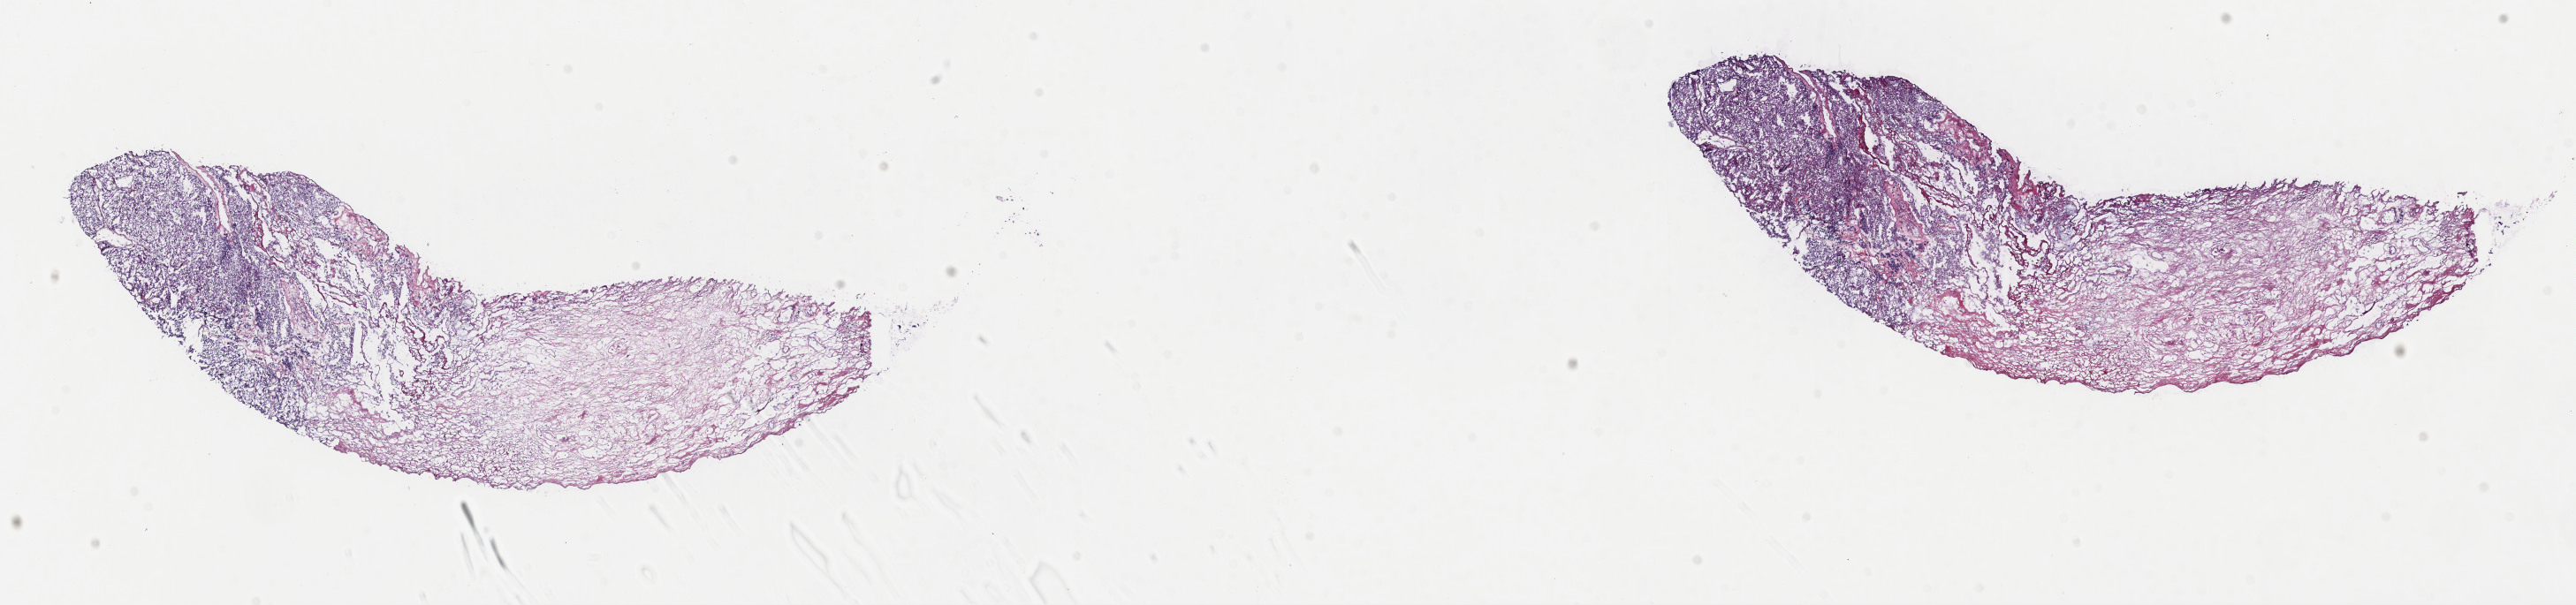
Whole-slide histology image, Hematoxylin and eosin (H&E) stained — low-resolution overview of the scanned area, about 23.0 x 5.4 mm (acquisition: 40x scan), frozen section from the top of the tissue portion, primary tumour sample from the kidney. Patient: male, age at initial diagnosis 48 years. Histologic grade: G3 (poorly differentiated). Slide review estimates, as recorded: tumour cells 50%, tumour nuclei 85%, normal cells 0%, stromal cells 50%, necrosis 0%. Infiltration values recorded for this section: lymphocyte infiltration 0%, monocyte infiltration 0%, neutrophil infiltration 0%.
AJCC pathologic stage: I (7th edition). Diagnosis: Renal cell carcinoma, NOS. Laterality: left.